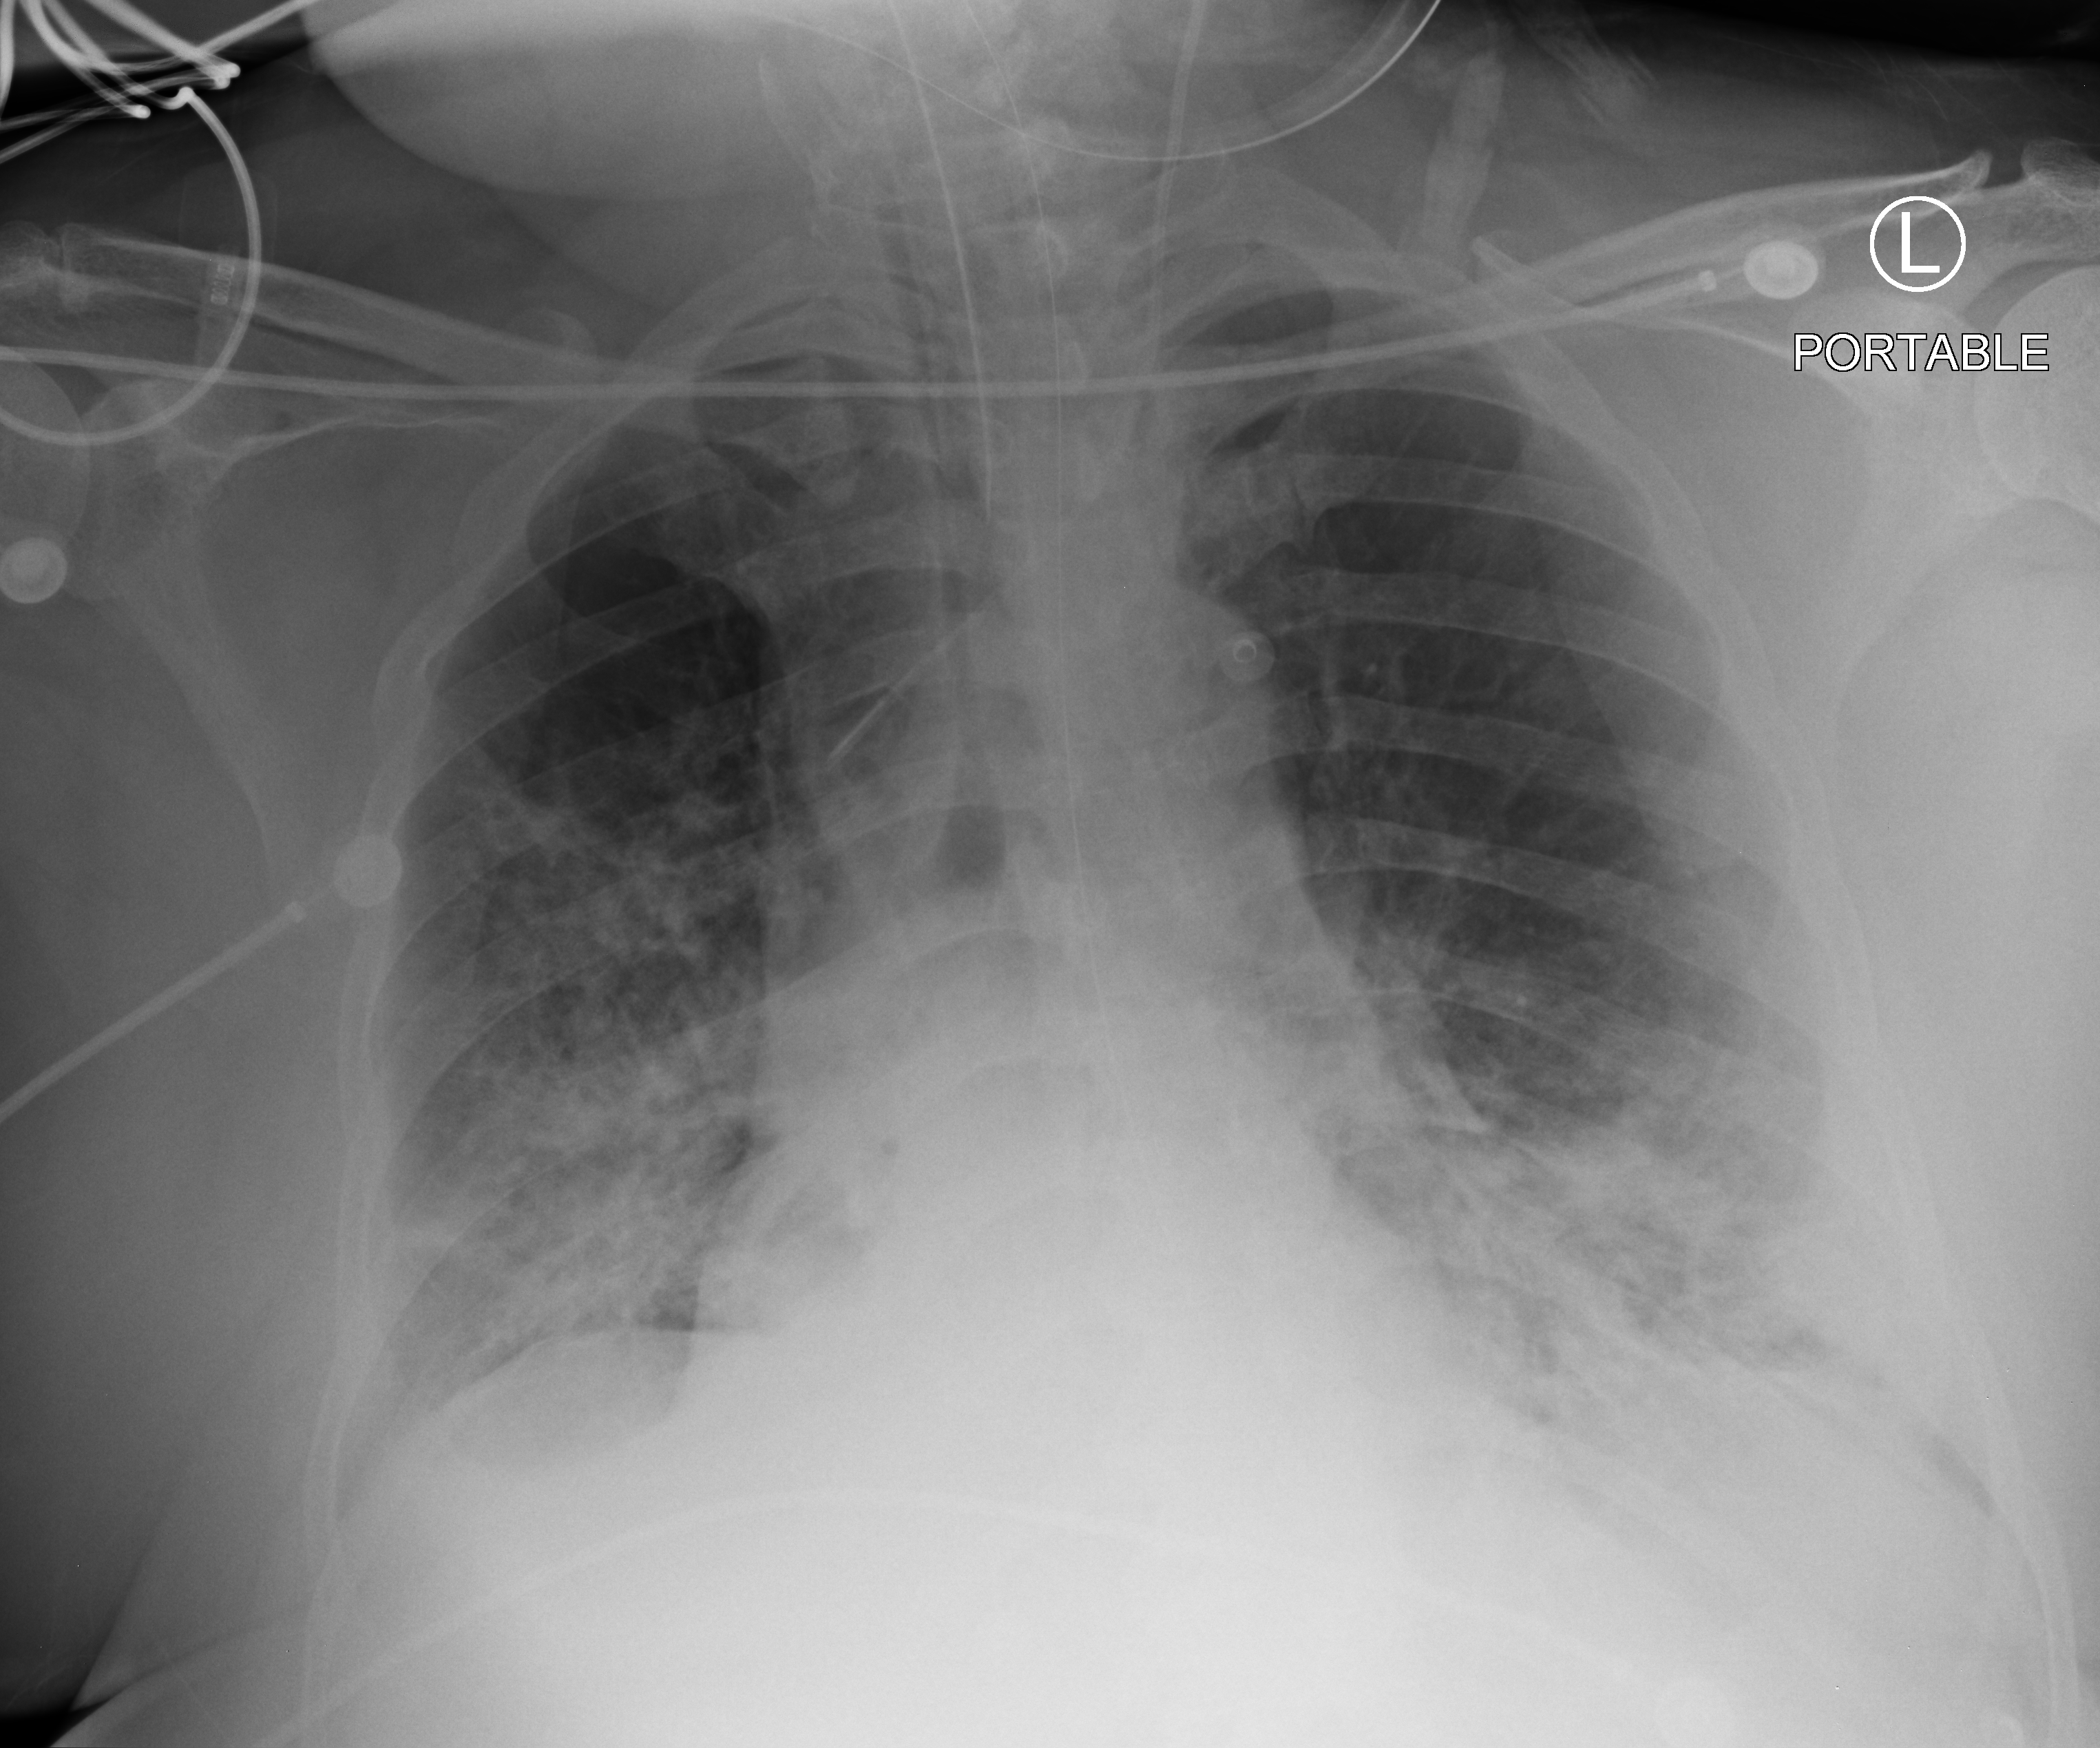
Portable chest radiograph, anteroposterior (AP) projection. Patient hospitalised with COVID-19, aged 18–59 years.
From the hospital-stay record, not from the radiograph (when in the stay this image was taken is not recorded): other chronic lung disease (admission record): yes; mechanically ventilated during this hospital stay: yes; admitted to intensive care during this hospital stay: yes.